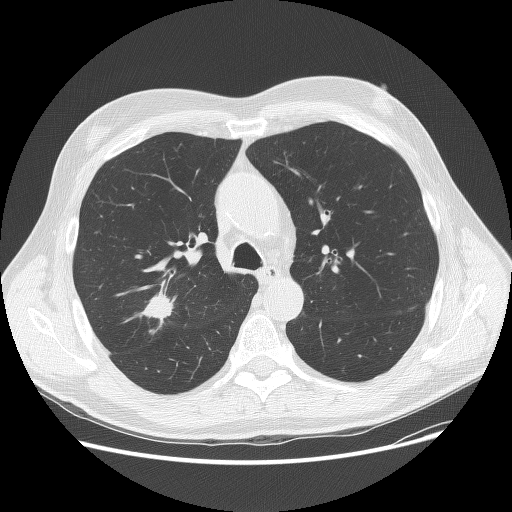
Axial slice from a low-dose chest CT screening exam; baseline annual screen; lung window (W 1500 / L -600 HU); 120 kVp; slice 52 of 156 in the series; 512 × 512 image matrix, field of view 380 × 380 mm. Male, age 70 years at enrolment. Current smoker at enrolment.
Expert-annotated lung lesion, bounding box <133,280,195,335> (left, top, right, bottom; pixels). The screening reader recorded 2 non-calcified nodules or masses ≥4 mm on this exam (right upper lobe, left lower lobe); which of them this box marks is not recorded. Later outcome: lung cancer diagnosed 15 days after this screen — adenocarcinoma, NOS, right upper lobe, poorly differentiated (G3), stage IIA (AJCC 6th edition), 23 mm at pathology.